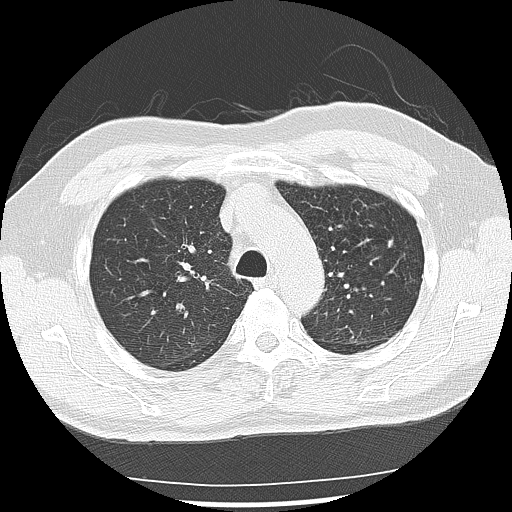
Low-dose screening chest CT, one axial slice; slice 101 of 142 in the series (ordered by position); reconstruction kernel LUNG; 120 kVp; lung window (W 1500 / L -600 HU); 2.5 mm slice thickness; 512 × 512 image matrix, field of view 360 × 360 mm.
Outlined on this slice (expert manual segmentation):
- lesion 2 (nodule, lower lobe of right lung): box from (x=249, y=336) to (x=269, y=361) px